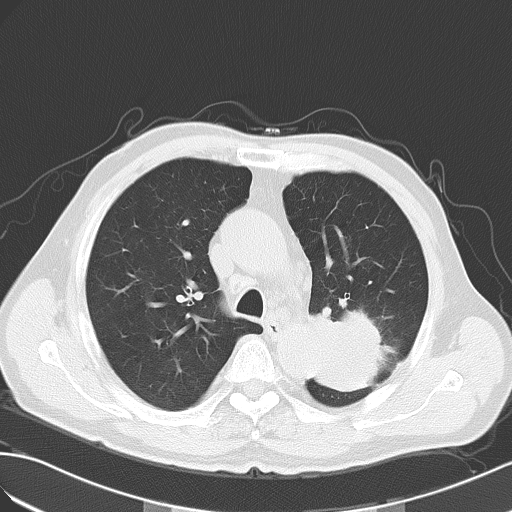
Chest CT, one axial slice. Slice 39 of 55 in the series (ordered by position). Reconstruction kernel B70f. Lung window (W 1500 / L -600 HU). 5 mm slice thickness. 512 × 512 image matrix. Patient: male, 63 years. Case-level facts recorded for this patient, not image findings: clinical TNM (as recorded): T3 N3 M1a; histopathological grade: G3.
Structures marked on this image (bounding box drawn by a radiologist):
- lung tumour (recorded histology: large cell carcinoma): bounding box [x1, y1, x2, y2] px = [300, 298, 387, 400]